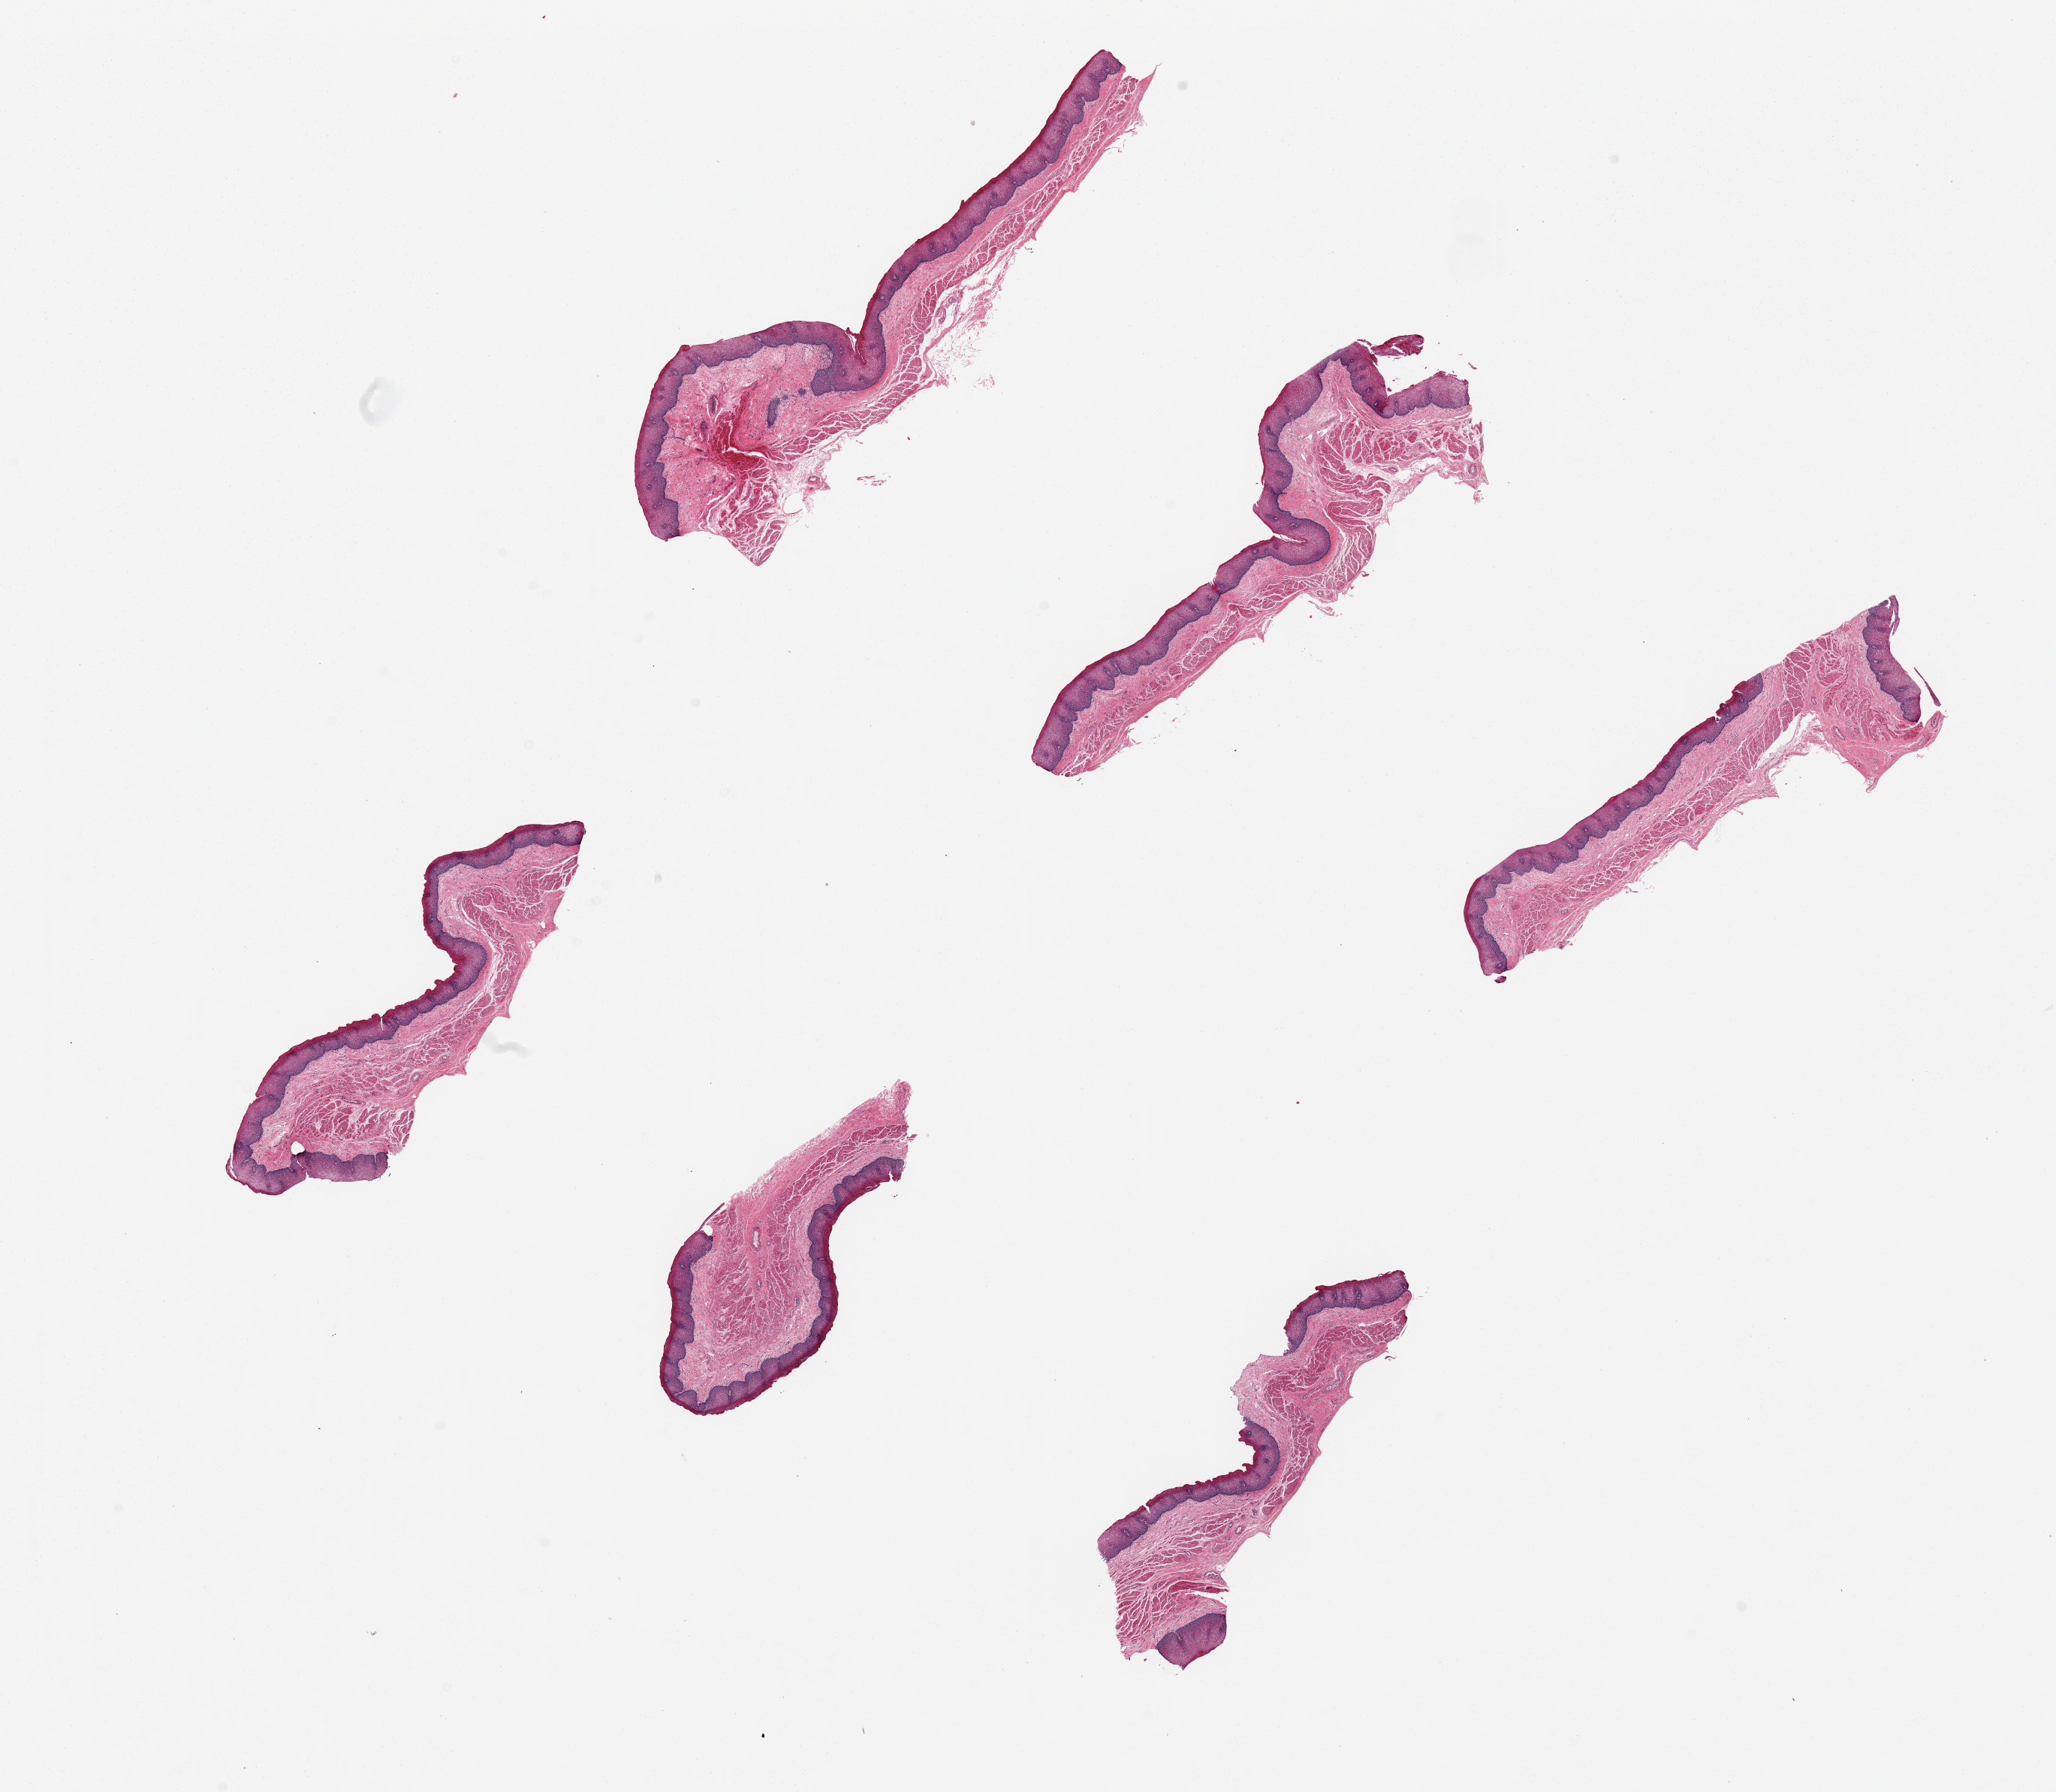
Digitized H&E-stained section, low-resolution overview of the scanned area, about 21.7 x 18.9 mm; PAXgene-fixed paraffin-embedded (PFPE) section; target tissue: esophageal mucous membrane; donor tissue sample. Donor: female.
Pathologist's review note for this sample: 6 pieces, squamous mucosa up to ~0.3mm thick.